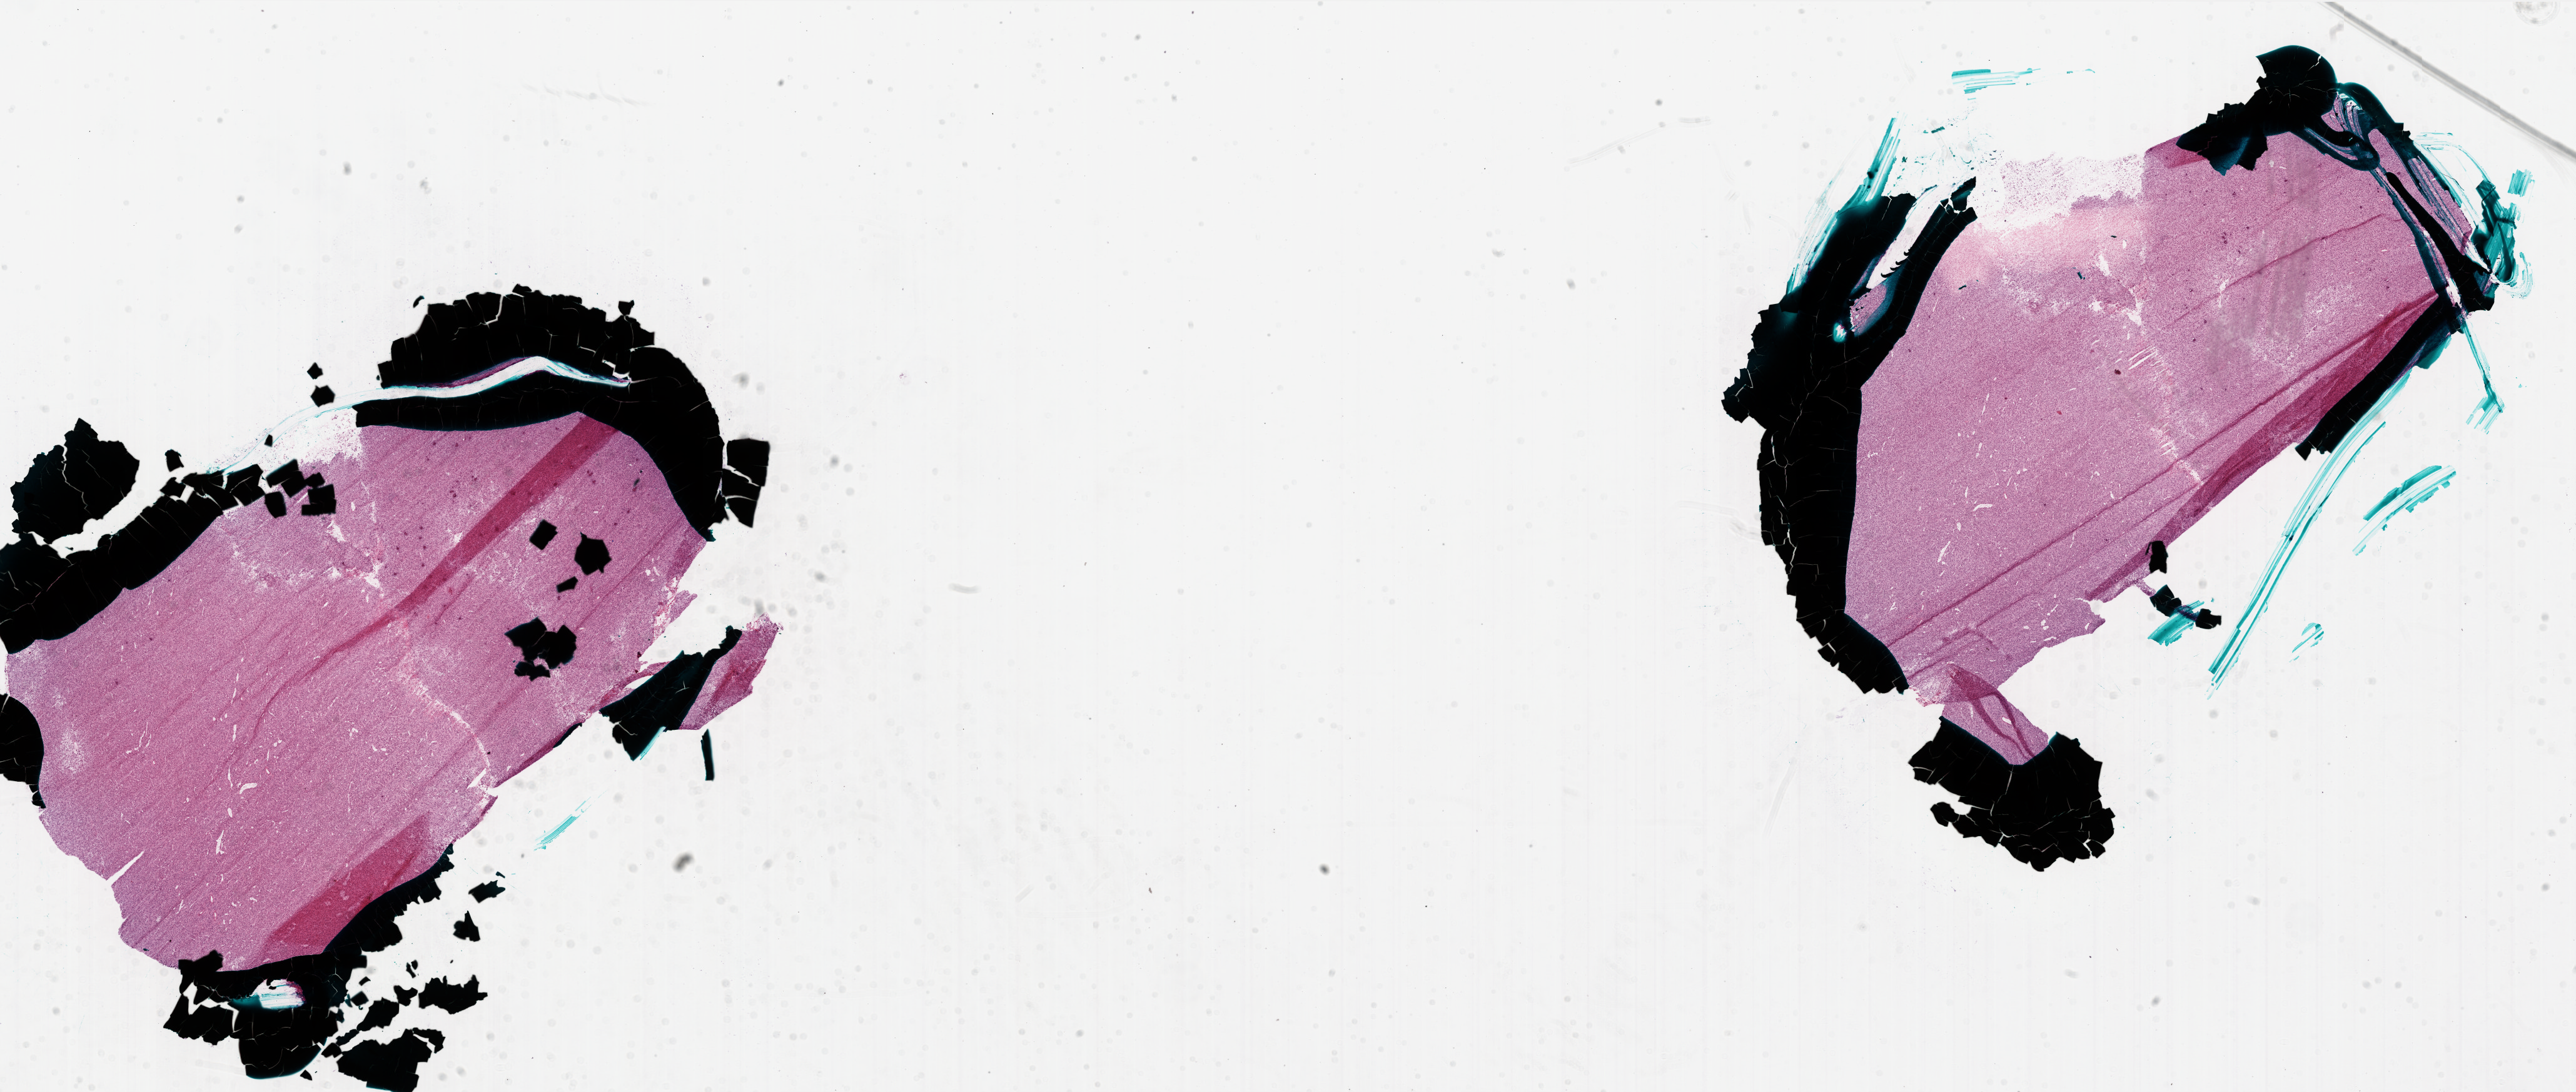
Whole-slide histology image, Hematoxylin and eosin (H&E) stained — whole scanned area (about 33.0 x 14.0 mm) shown as a low-resolution overview; frozen section; primary tumour sample from the brain. Patient: female, age at initial diagnosis 53 years.
Diagnosis: Glioblastoma.